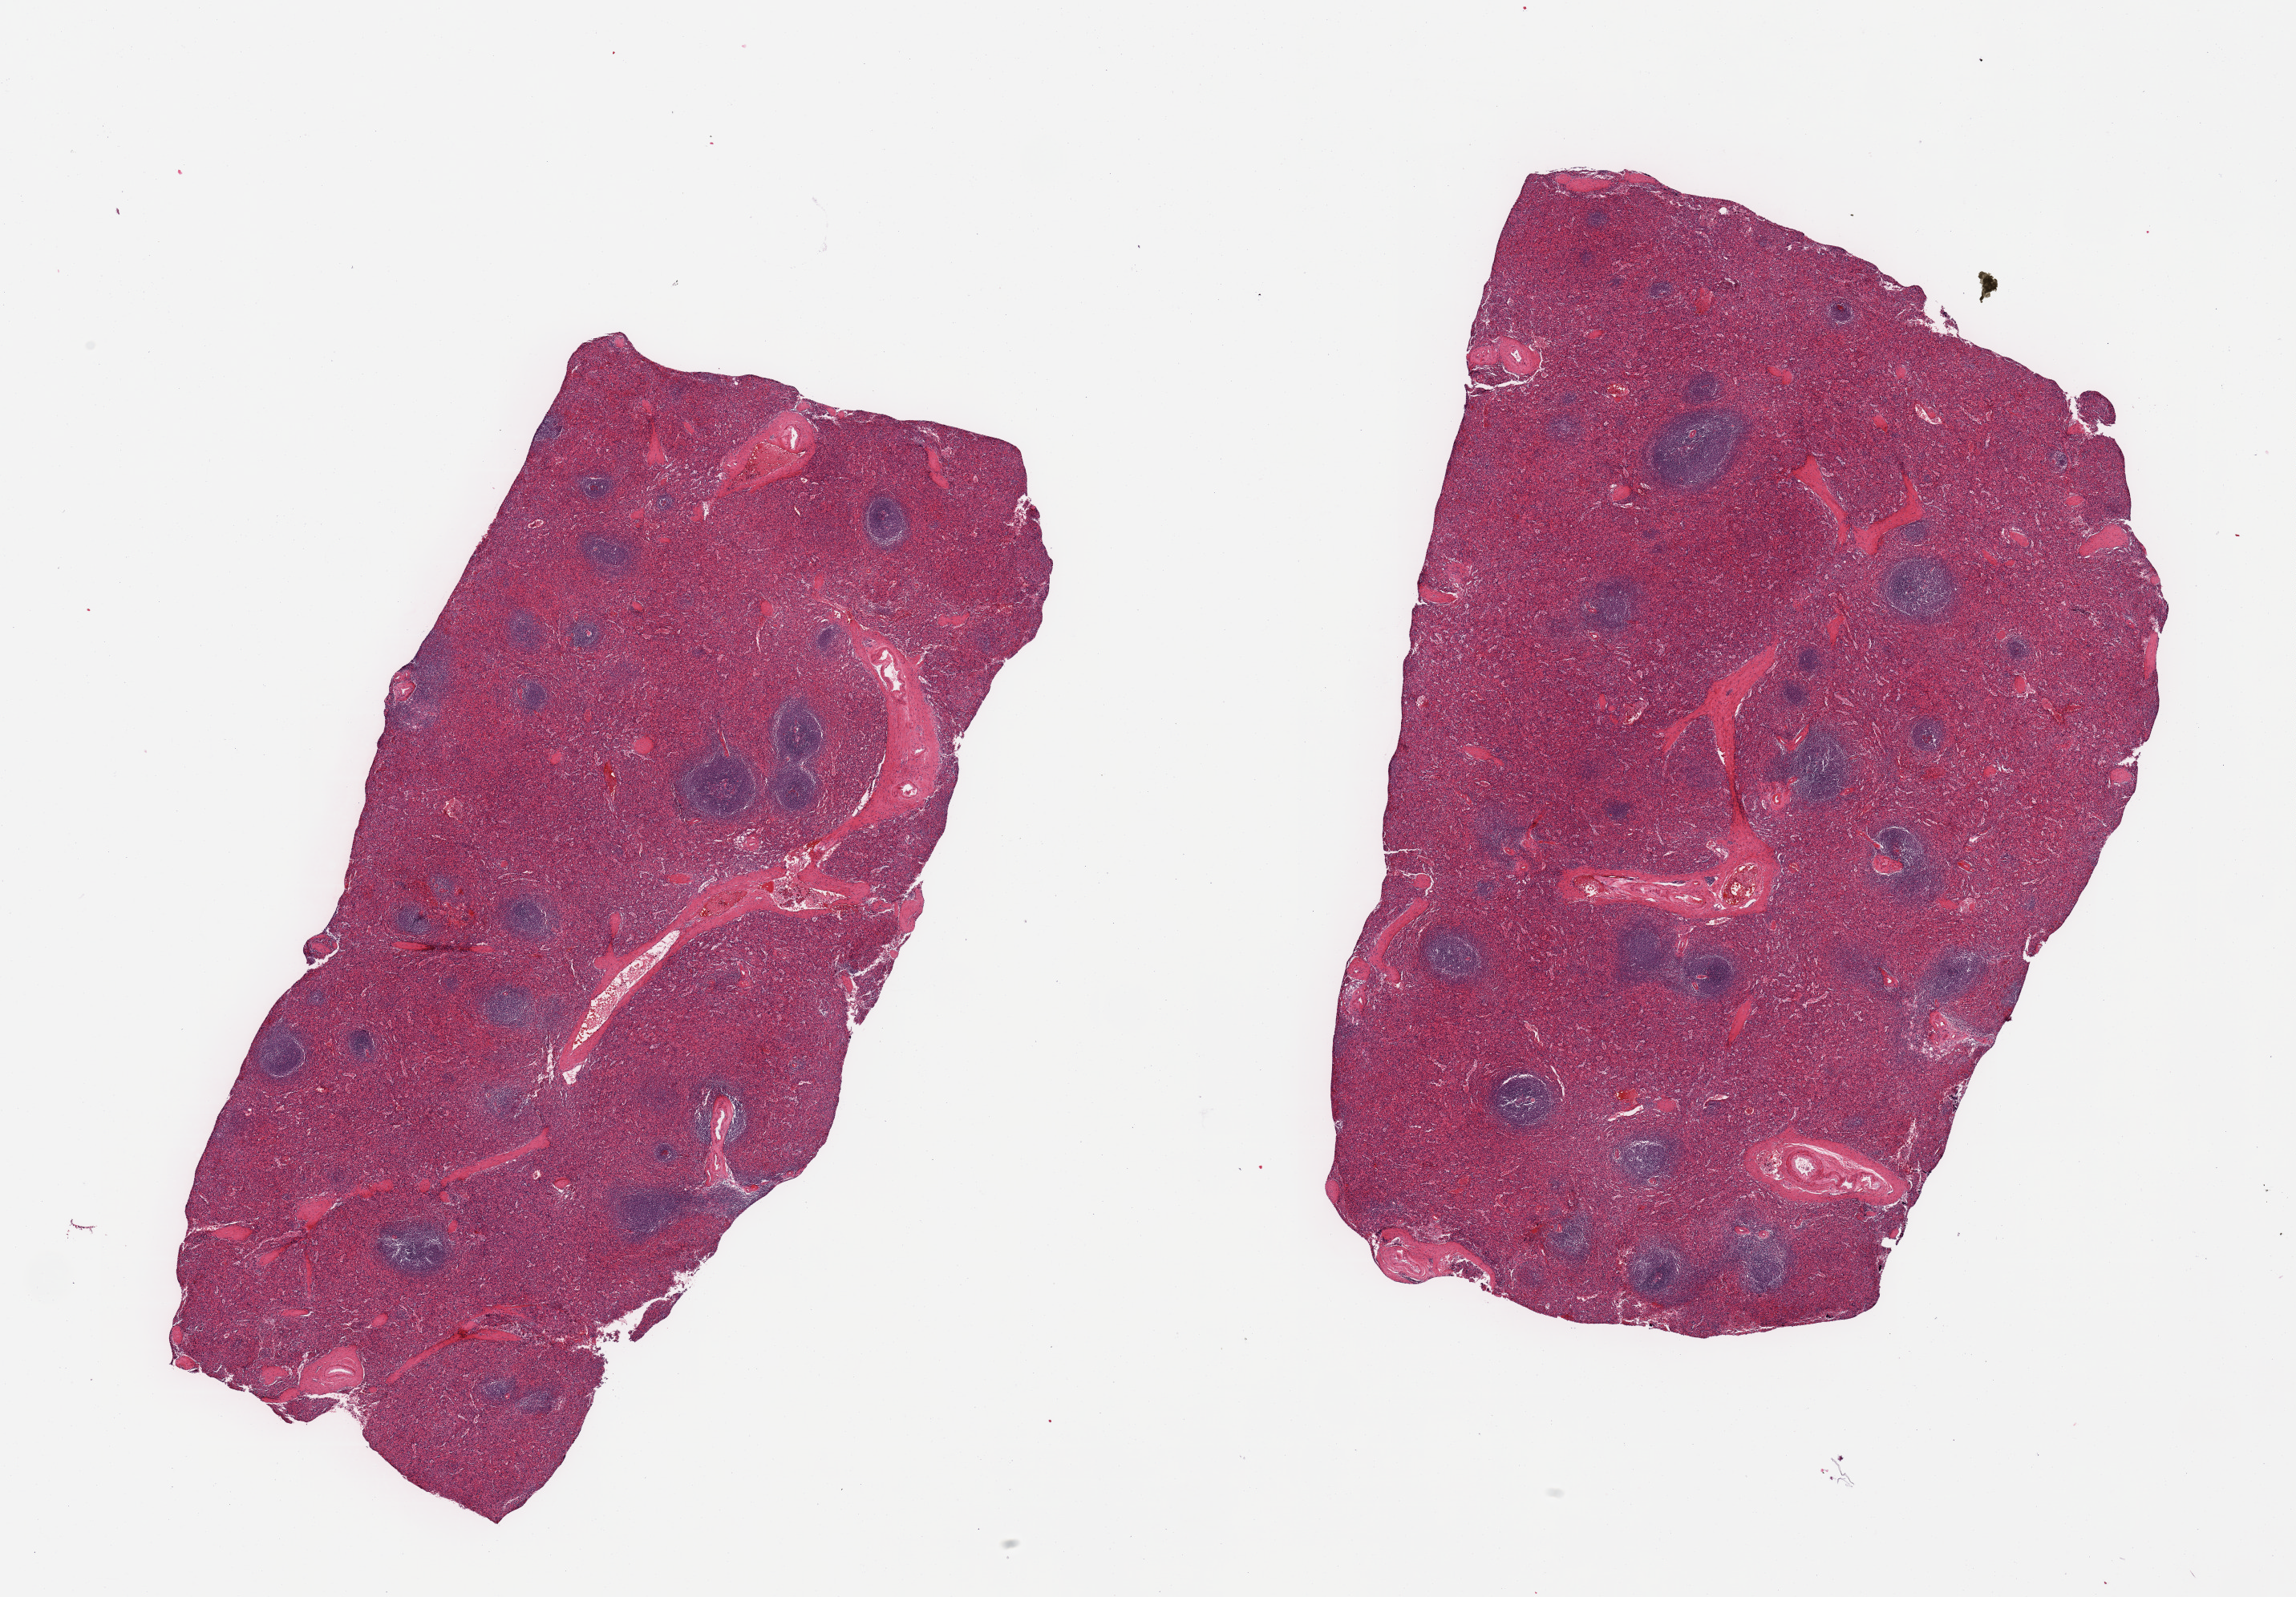
Digitized hematoxylin and eosin (H&E)-stained section — shown as a low-resolution overview of the whole scanned area (about 22.6 x 15.8 mm); PAXgene-fixed paraffin-embedded (PFPE) section; section of spleen (target tissue); donor tissue sample. Donor sex: female.
Pathologist's review note for this sample: 2 pieces; minimal congestion; well defined lymphoid tissue.